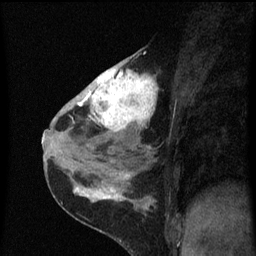
Breast MRI (dynamic contrast-enhanced), one sagittal slice. Position 33 of 60 along the scan axis. Dynamic contrast-enhanced series, image 2 of 3 at this slice position (ordered by acquisition). 1.5 T. TE 4.2 ms, TR 8 ms. 256 × 256 image matrix, field of view 180 × 180 mm. Patient: female, 38 years.
Outlined on this slice (semi-automatic segmentation, software-assisted and operator-edited):
- analysis volume of interest (the breast-tissue region the enhancement analysis was run in; not a lesion): bounding box [x1, y1, x2, y2] px = [80, 54, 159, 151]
- tumour enhancement mask (voxels above the 70 % enhancement threshold inside the analysis volume of interest): [80, 60, 159, 133]